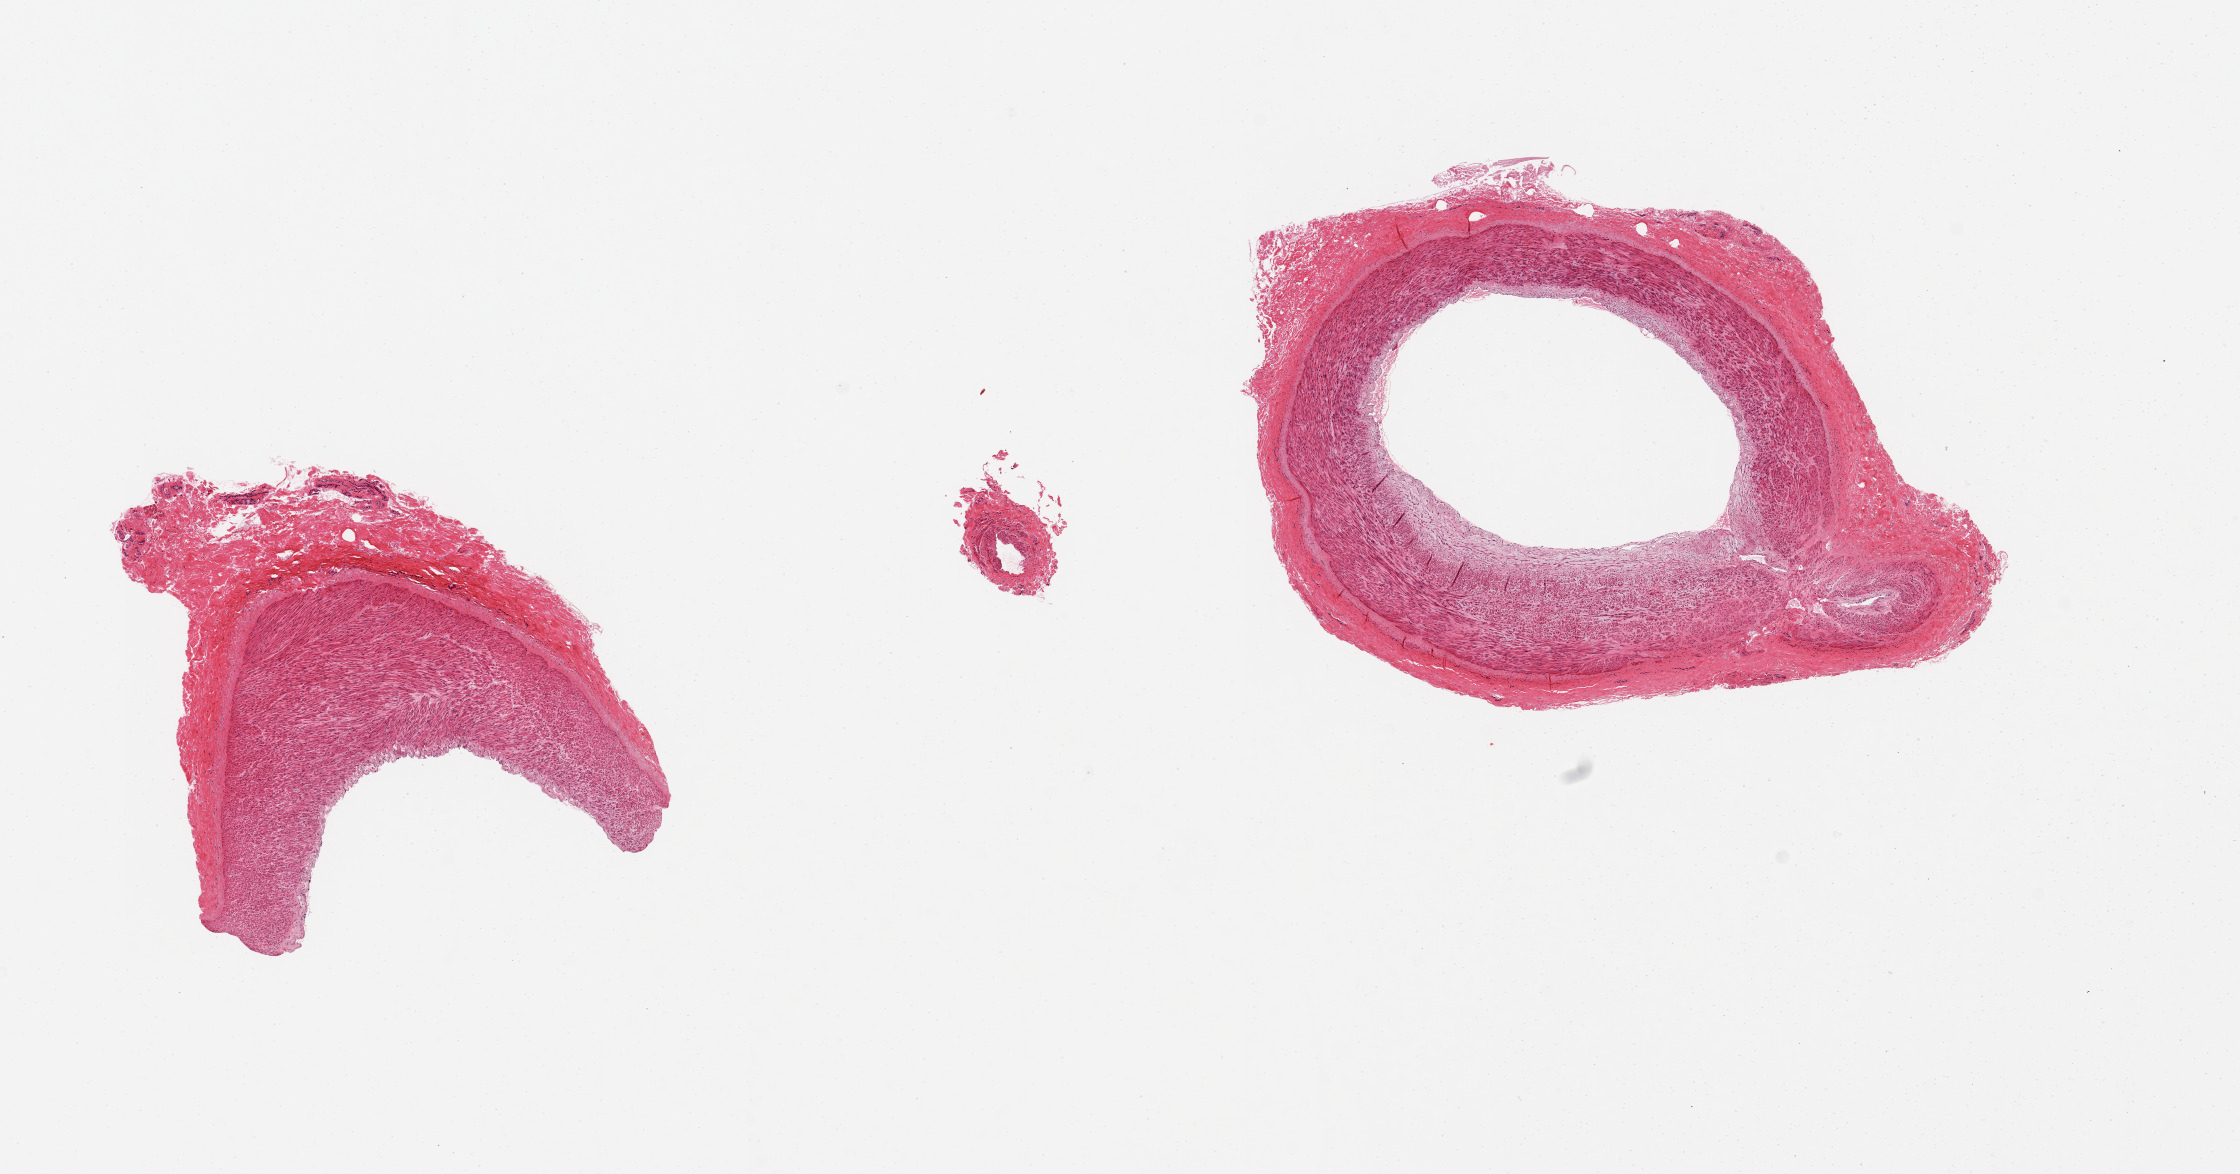
Whole-slide image, hematoxylin and eosin (H&E) stain, whole scanned area (about 17.7 x 9.3 mm, from a 20x scan) shown as a low-resolution overview. PAXgene-fixed paraffin-embedded (PFPE) section. Section of tibial artery (target tissue). Donor tissue sample. Donor sex: female.
Review note (as recorded): 2 pieces, circumferential adherent fibrous tissue ~0.5mm.